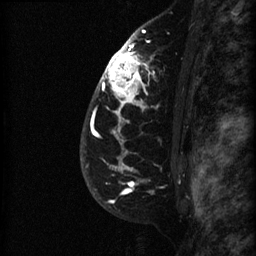
Breast MRI (dynamic contrast-enhanced), one sagittal slice. Position 50 of 60 along the scan axis. Dynamic contrast-enhanced series, image 2 of 3 at this slice position (ordered by acquisition). 1.5 T. TE 4.2 ms, TR 22.7 ms. 1.5 mm slice thickness. 256 × 256 image matrix. Female patient, age 48 years. Case-level facts recorded for this patient, not image findings: setting: breast cancer imaged before/during neoadjuvant chemotherapy; receptor status: triple-negative.
Structures marked on this image (semi-automatically segmented with operator editing):
- analysis volume of interest (the breast-tissue region the enhancement analysis was run in; not a lesion): bounding box (x1, y1, x2, y2) in pixels: (89, 27, 191, 180)
- tumour enhancement mask (voxels above the 90 % enhancement threshold inside the analysis volume of interest): (92, 30, 149, 171)